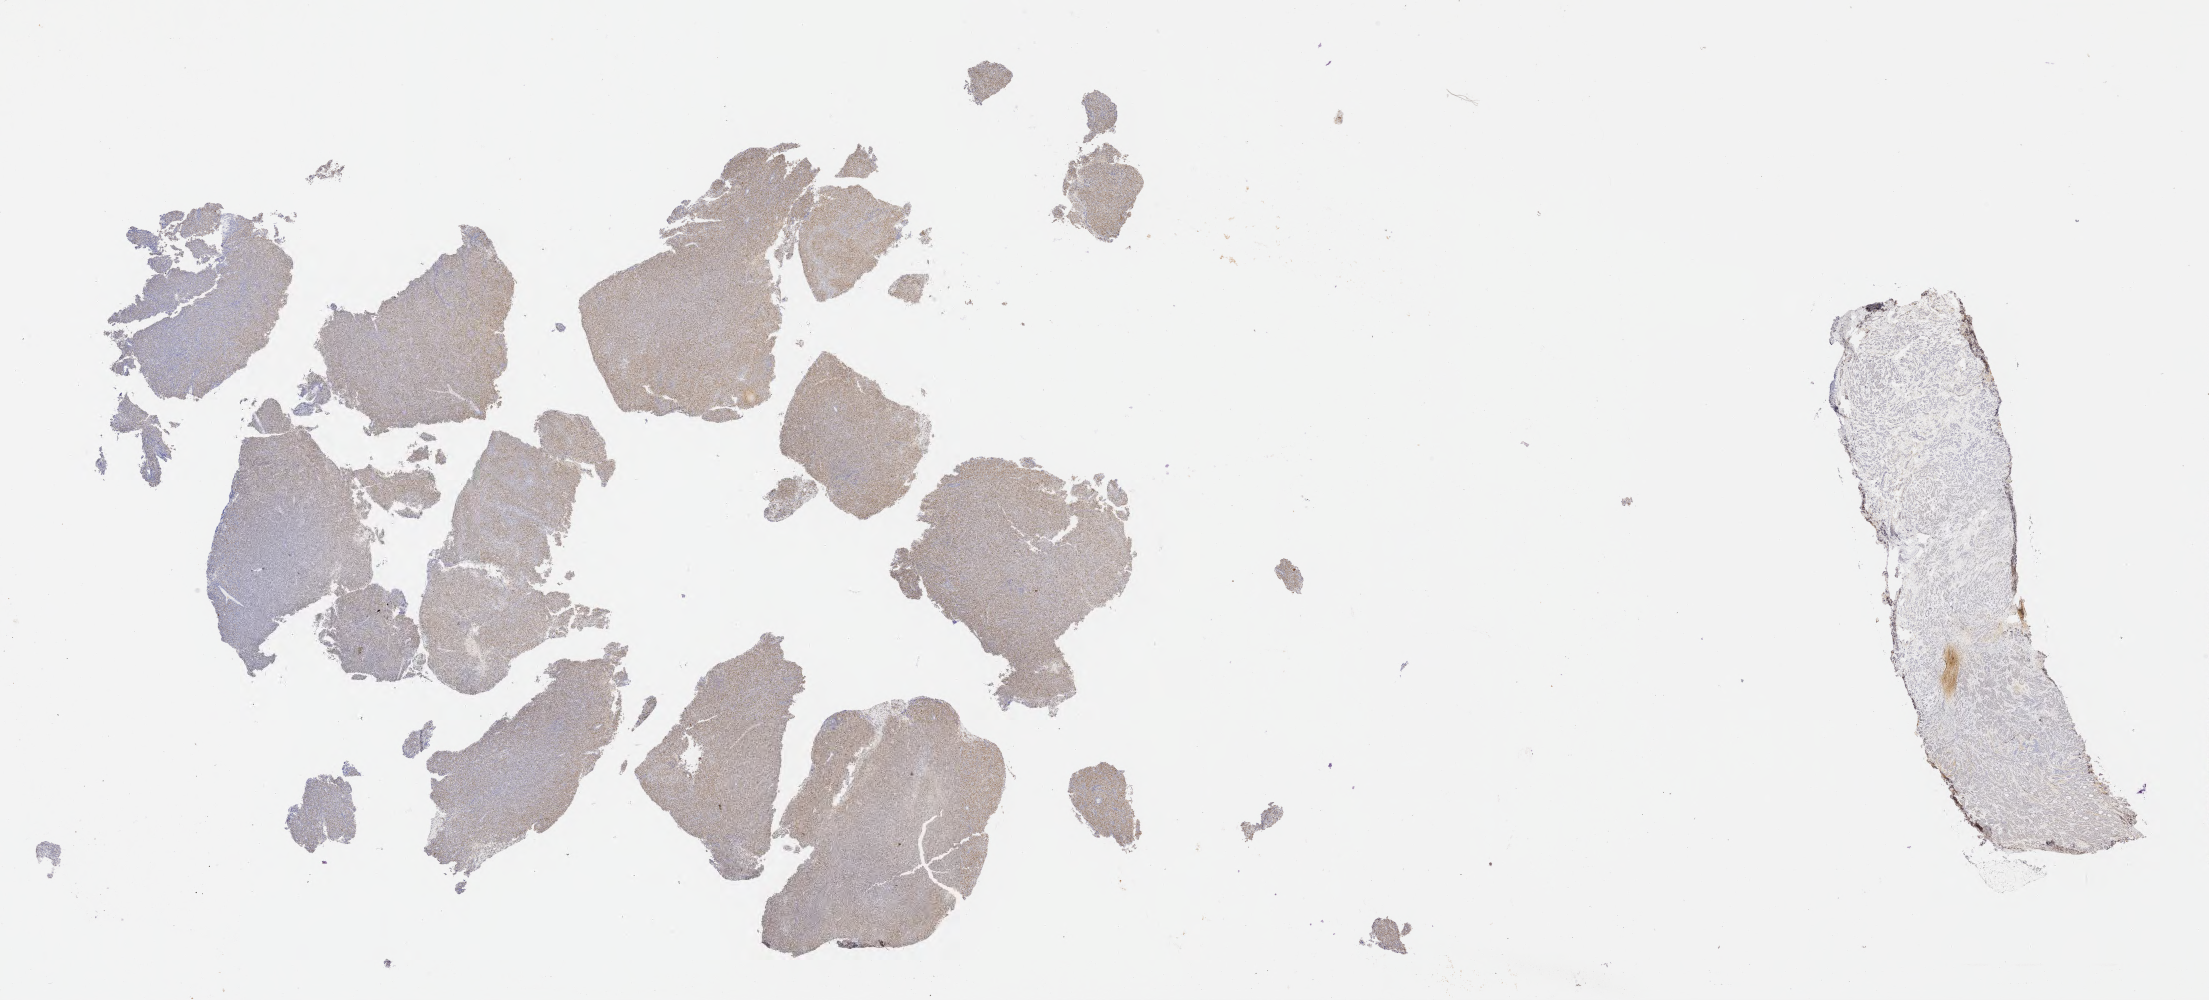
Immunohistochemistry (IHC) whole-slide image stained for p53 — shown as a low-resolution overview of the whole scanned area (about 35.7 x 16.2 mm). Specimen: tumor tissue. Site: lymph node. Patient female; 50 years old.
* histologic diagnosis: Diffuse large B-cell lymphoma, NOS